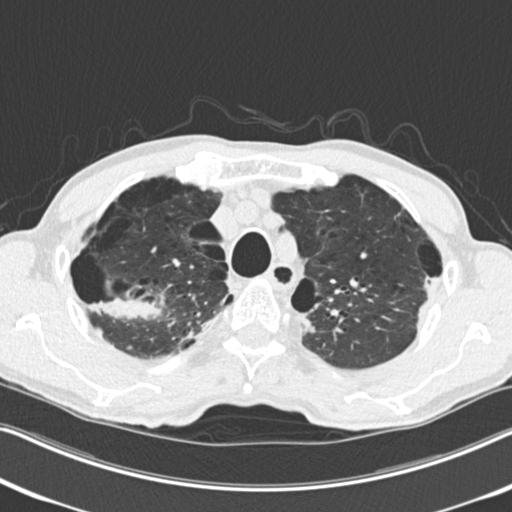
Low-dose screening chest CT, one axial slice; slice 200 of 251 in the series (ordered by position); reconstruction kernel B30f; lung window (W 1500 / L -600 HU); 2 mm slice thickness; 512 × 512 image matrix.
Annotated regions visible in this slice (outlined manually by an expert reader):
- lesion 1 (tumor, upper lobe of right lung): bounding box <86,297,161,320> (left, top, right, bottom; pixels)